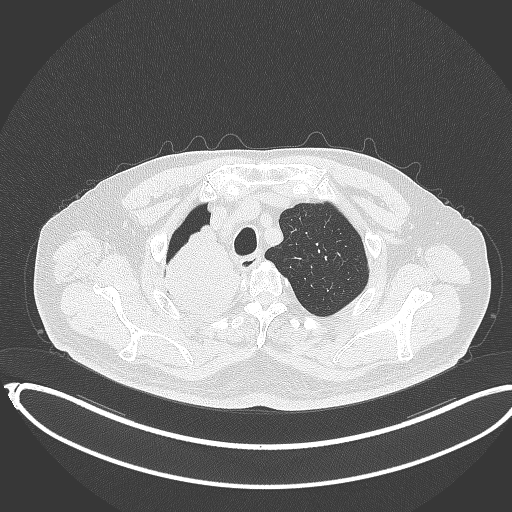
Chest CT, one axial slice; position 314 of 403 along the scan axis; reconstruction kernel B70f; 120 kVp; lung window (W 1500 / L -600 HU); 512 × 512 image matrix. Patient: male, 68 years. From the clinical record (not read from this slice): clinical TNM (as recorded): T2a N0 M0.
Annotated regions visible in this slice (bounding box drawn by a radiologist):
- lung tumour (recorded histology: adenocarcinoma): bounding box (x1, y1, x2, y2) in pixels: (158, 222, 244, 320)